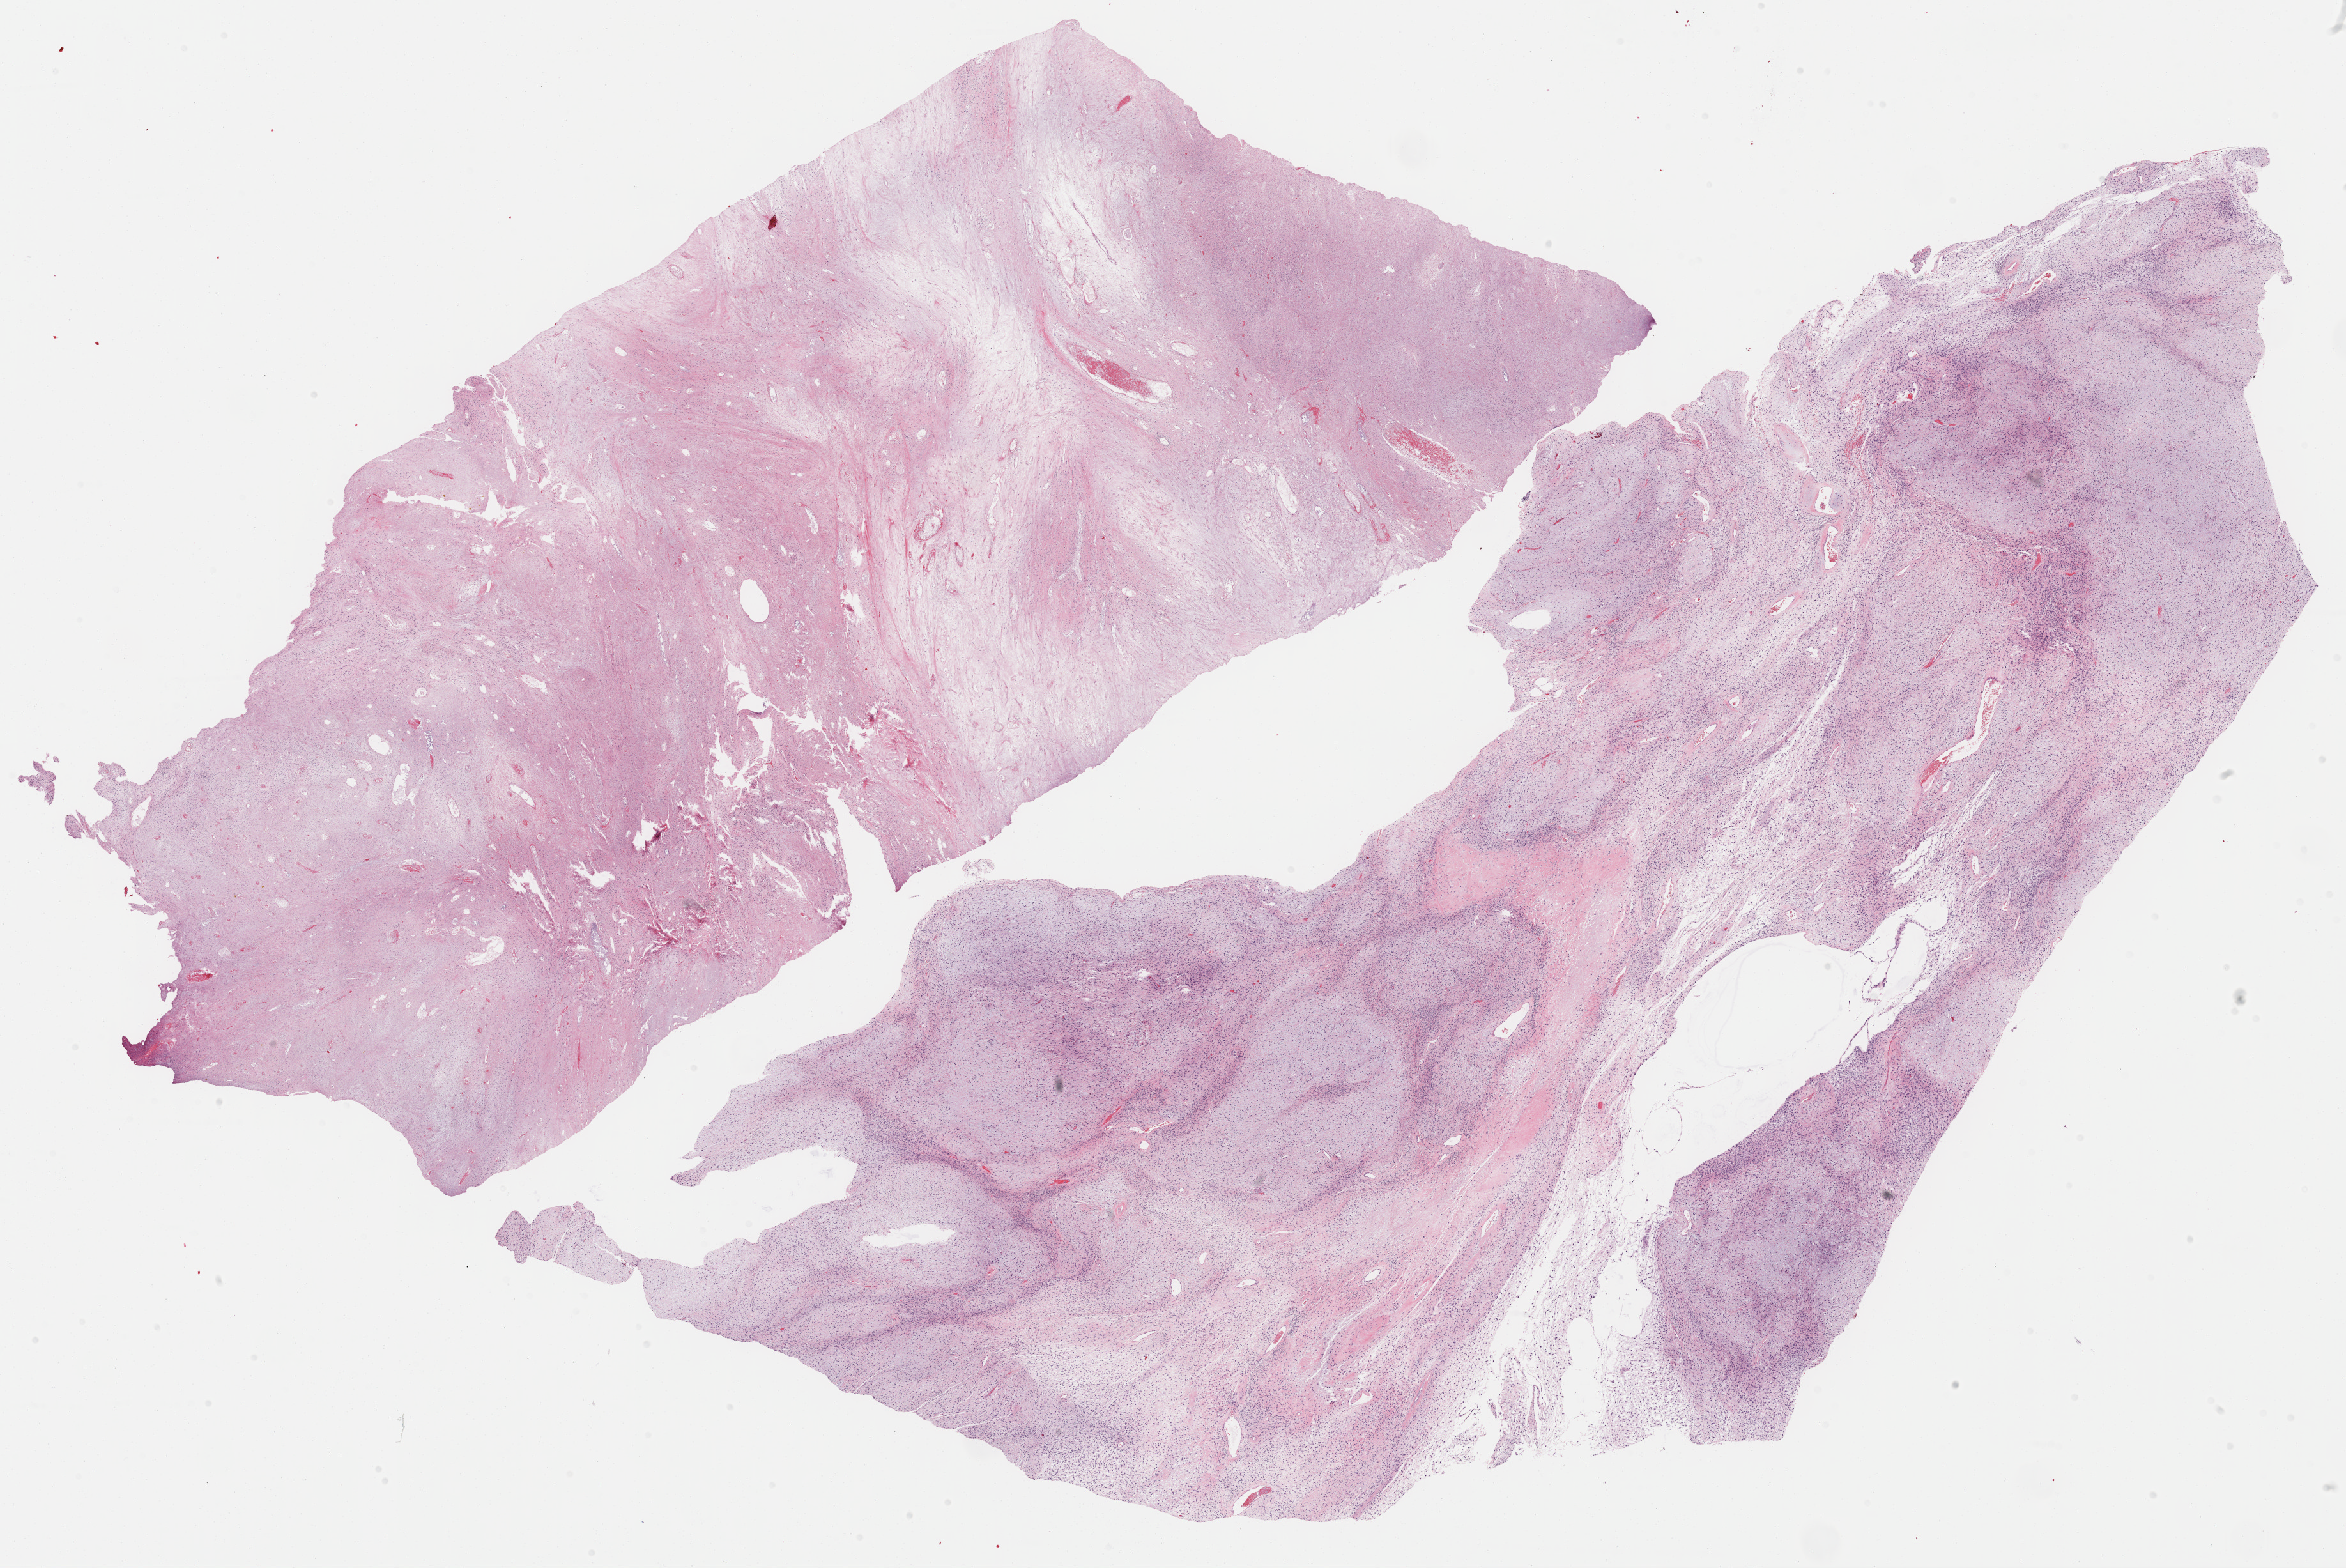
Whole-slide histology image, Hematoxylin and eosin (H&E) stained — low-resolution overview of the scanned area, about 29.7 x 19.8 mm (from a 40x scan). Formalin-fixed paraffin-embedded (FFPE) diagnostic section. Retroperitoneum and peritoneum, primary tumour sample. Male patient; age at initial diagnosis 52 years.
Histologic diagnosis: Undifferentiated sarcoma.